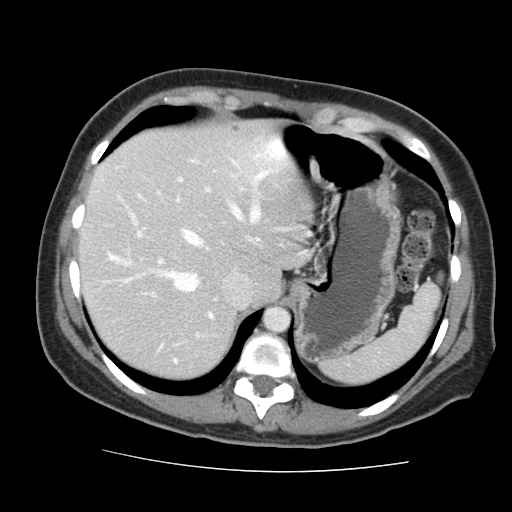
Contrast-enhanced abdominal CT, one axial slice; slice 116 of 144 in the series (ordered by position); 120 kVp; soft-tissue window (W 400 / L 40 HU); 2.5 mm slice thickness; 512 × 512 image matrix. Female patient, age 46 years. From the clinical record (not read from this slice): diagnosis: colorectal cancer liver metastases, imaged before liver resection; multiple liver metastases: no; largest metastasis: 2.8 cm; disease in both lobes: no.
Annotated regions visible in this slice (manually delineated by an expert):
- hepatic veins: bounding box (x1, y1, x2, y2) in pixels: (109, 171, 267, 292)
- liver: (81, 124, 309, 378)
- planned liver remnant (the part of the liver to remain after resection): (81, 124, 309, 378)
- portal vein (with intrahepatic branches): (107, 175, 243, 363)